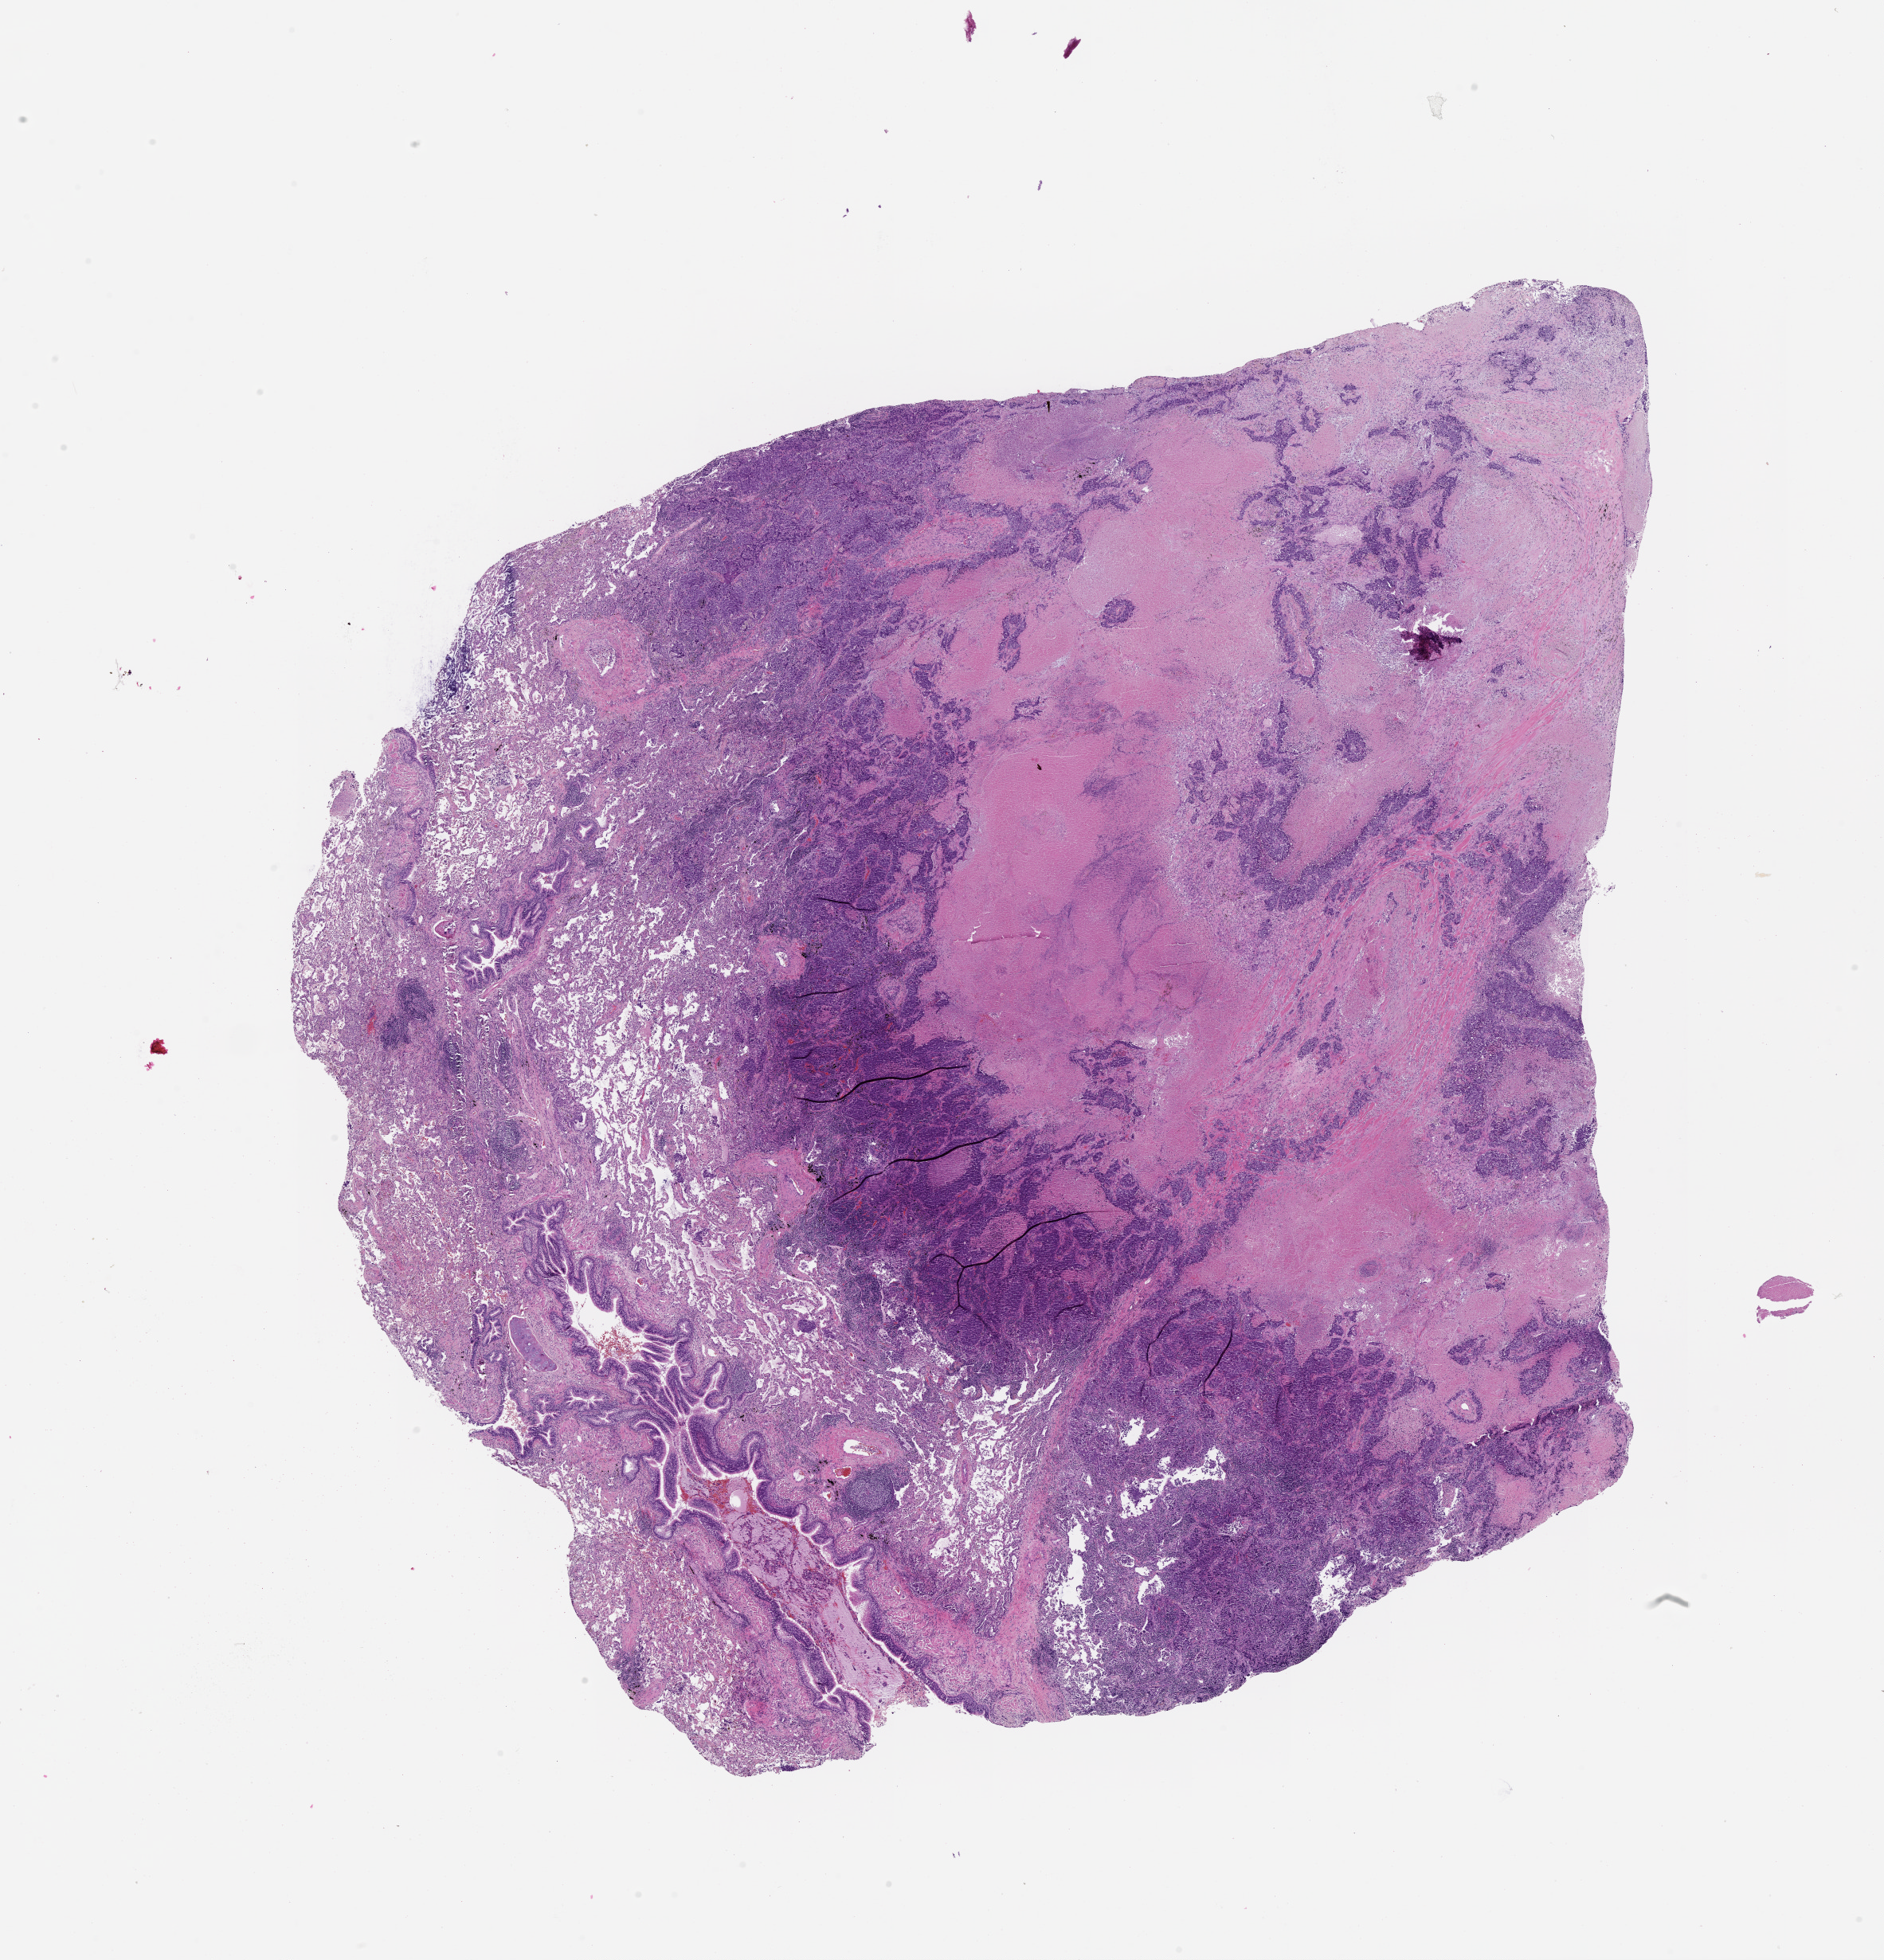
Whole-slide histology image, H&E, whole scanned area (about 19.0 x 19.8 mm, from a 20x scan) shown as a low-resolution overview; lung, tumour tissue. Patient: male, age 60 years.
Patient diagnosis (cohort enrolment): squamous cell carcinoma (lung).